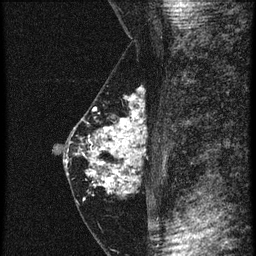
Breast MRI (dynamic contrast-enhanced), one sagittal slice. Position 24 of 60 along the scan axis. 4 images stored at this slice position (order not interpretable as contrast timing). 1.5 T. TE 4.2 ms, TR 20.4 ms. 1.5 mm slice thickness. 256 × 256 image matrix, field of view 180 × 180 mm. Patient: female, 46 years. Case-level facts recorded for this patient, not image findings: setting: breast cancer imaged before/during neoadjuvant chemotherapy; receptor status: triple-negative.
Structures marked on this image (semi-automatically segmented with operator editing):
- analysis volume of interest (the breast-tissue region the enhancement analysis was run in; not a lesion): box from (x=67, y=90) to (x=147, y=201) px
- tumour enhancement mask (voxels above the 90 % enhancement threshold inside the analysis volume of interest): (x=67, y=112)–(x=144, y=189)